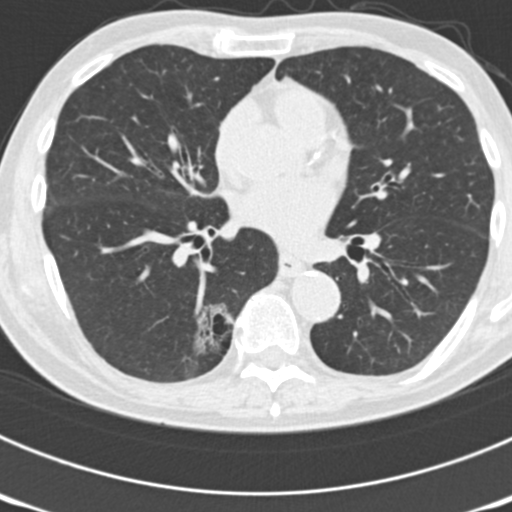
Low-dose screening chest CT, axial slice; third annual screen; lung window (W 1500 / L -600 HU); 2 mm slice thickness; standard (soft-tissue) reconstruction kernel (B30f); slice 85 of 177 in the series; 512 × 512 image matrix. Male participant, aged 70 years at enrolment. Current smoker at enrolment.
Expert reader's lesion annotation, bounding box (x1, y1, x2, y2) in pixels: (149, 301, 239, 385). The screening reader recorded 3 non-calcified nodules or masses ≥4 mm on this exam; which of them this box marks is not recorded.